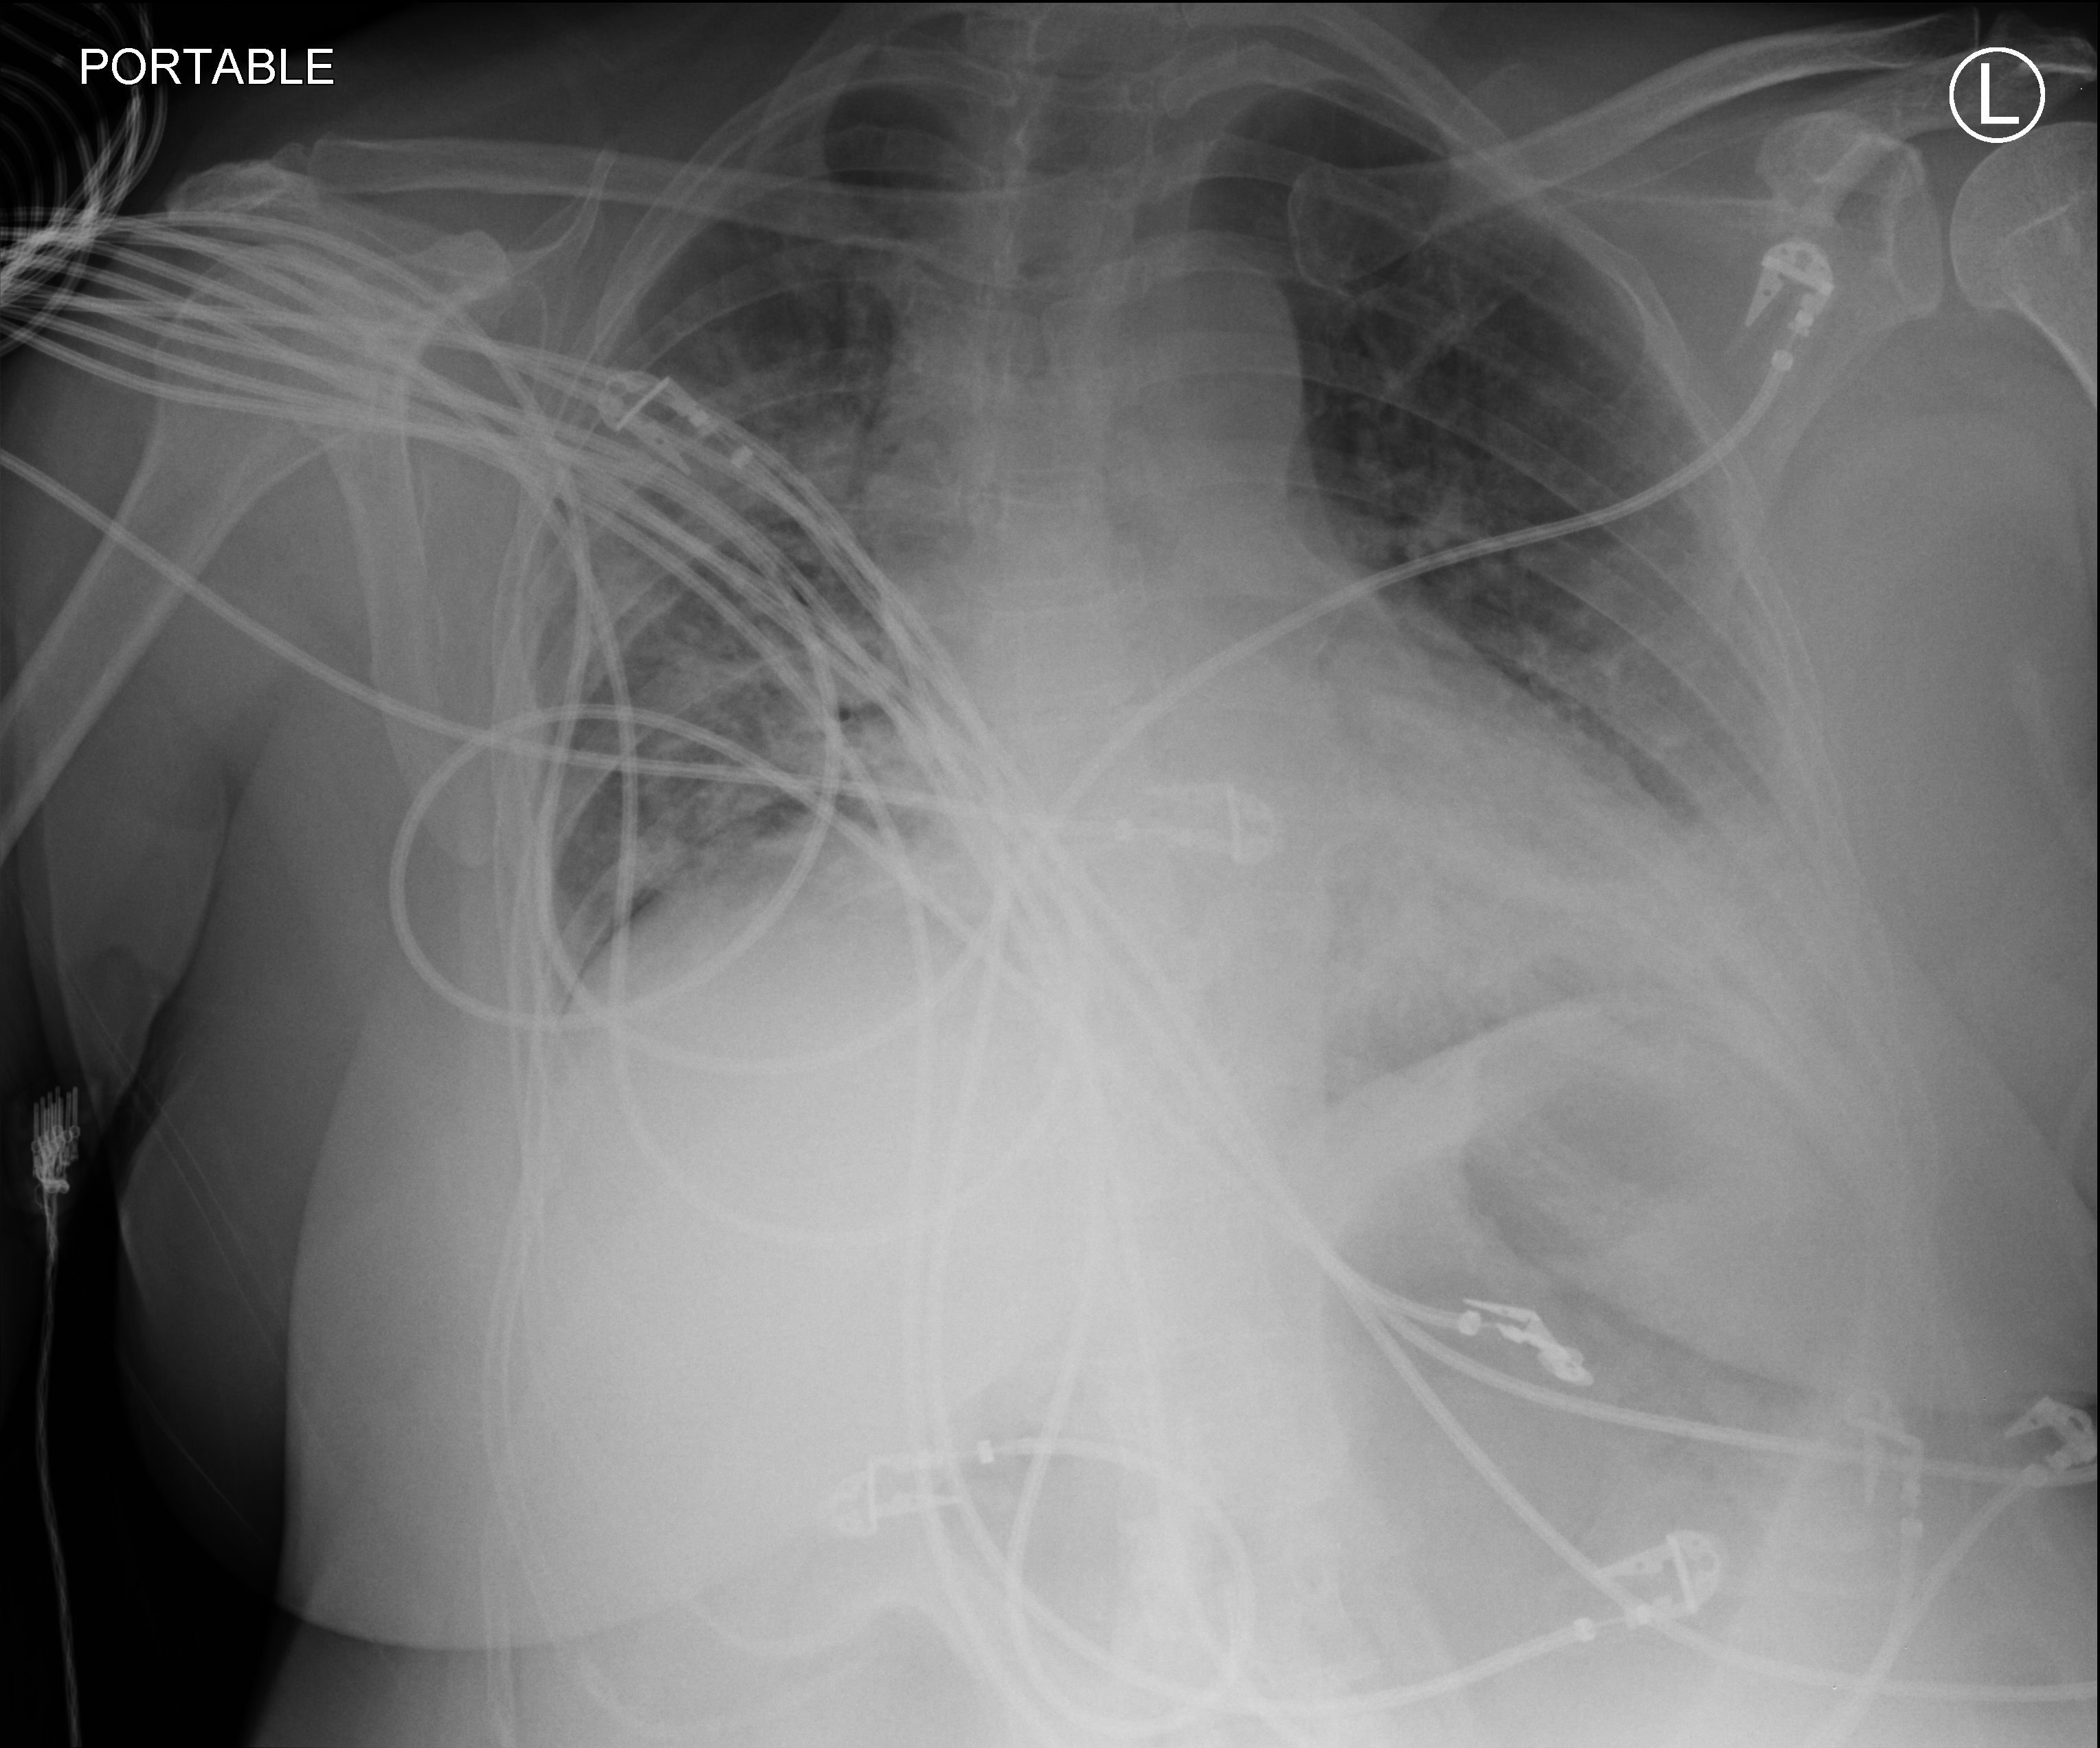
Bedside chest radiograph (computed radiography); anteroposterior (AP) projection. Female patient hospitalised with COVID-19, age 18–59 years.
Hospital-stay facts (about this admission, not read from this image; timing relative to this image not recorded): admitted to intensive care during this hospital stay: yes.